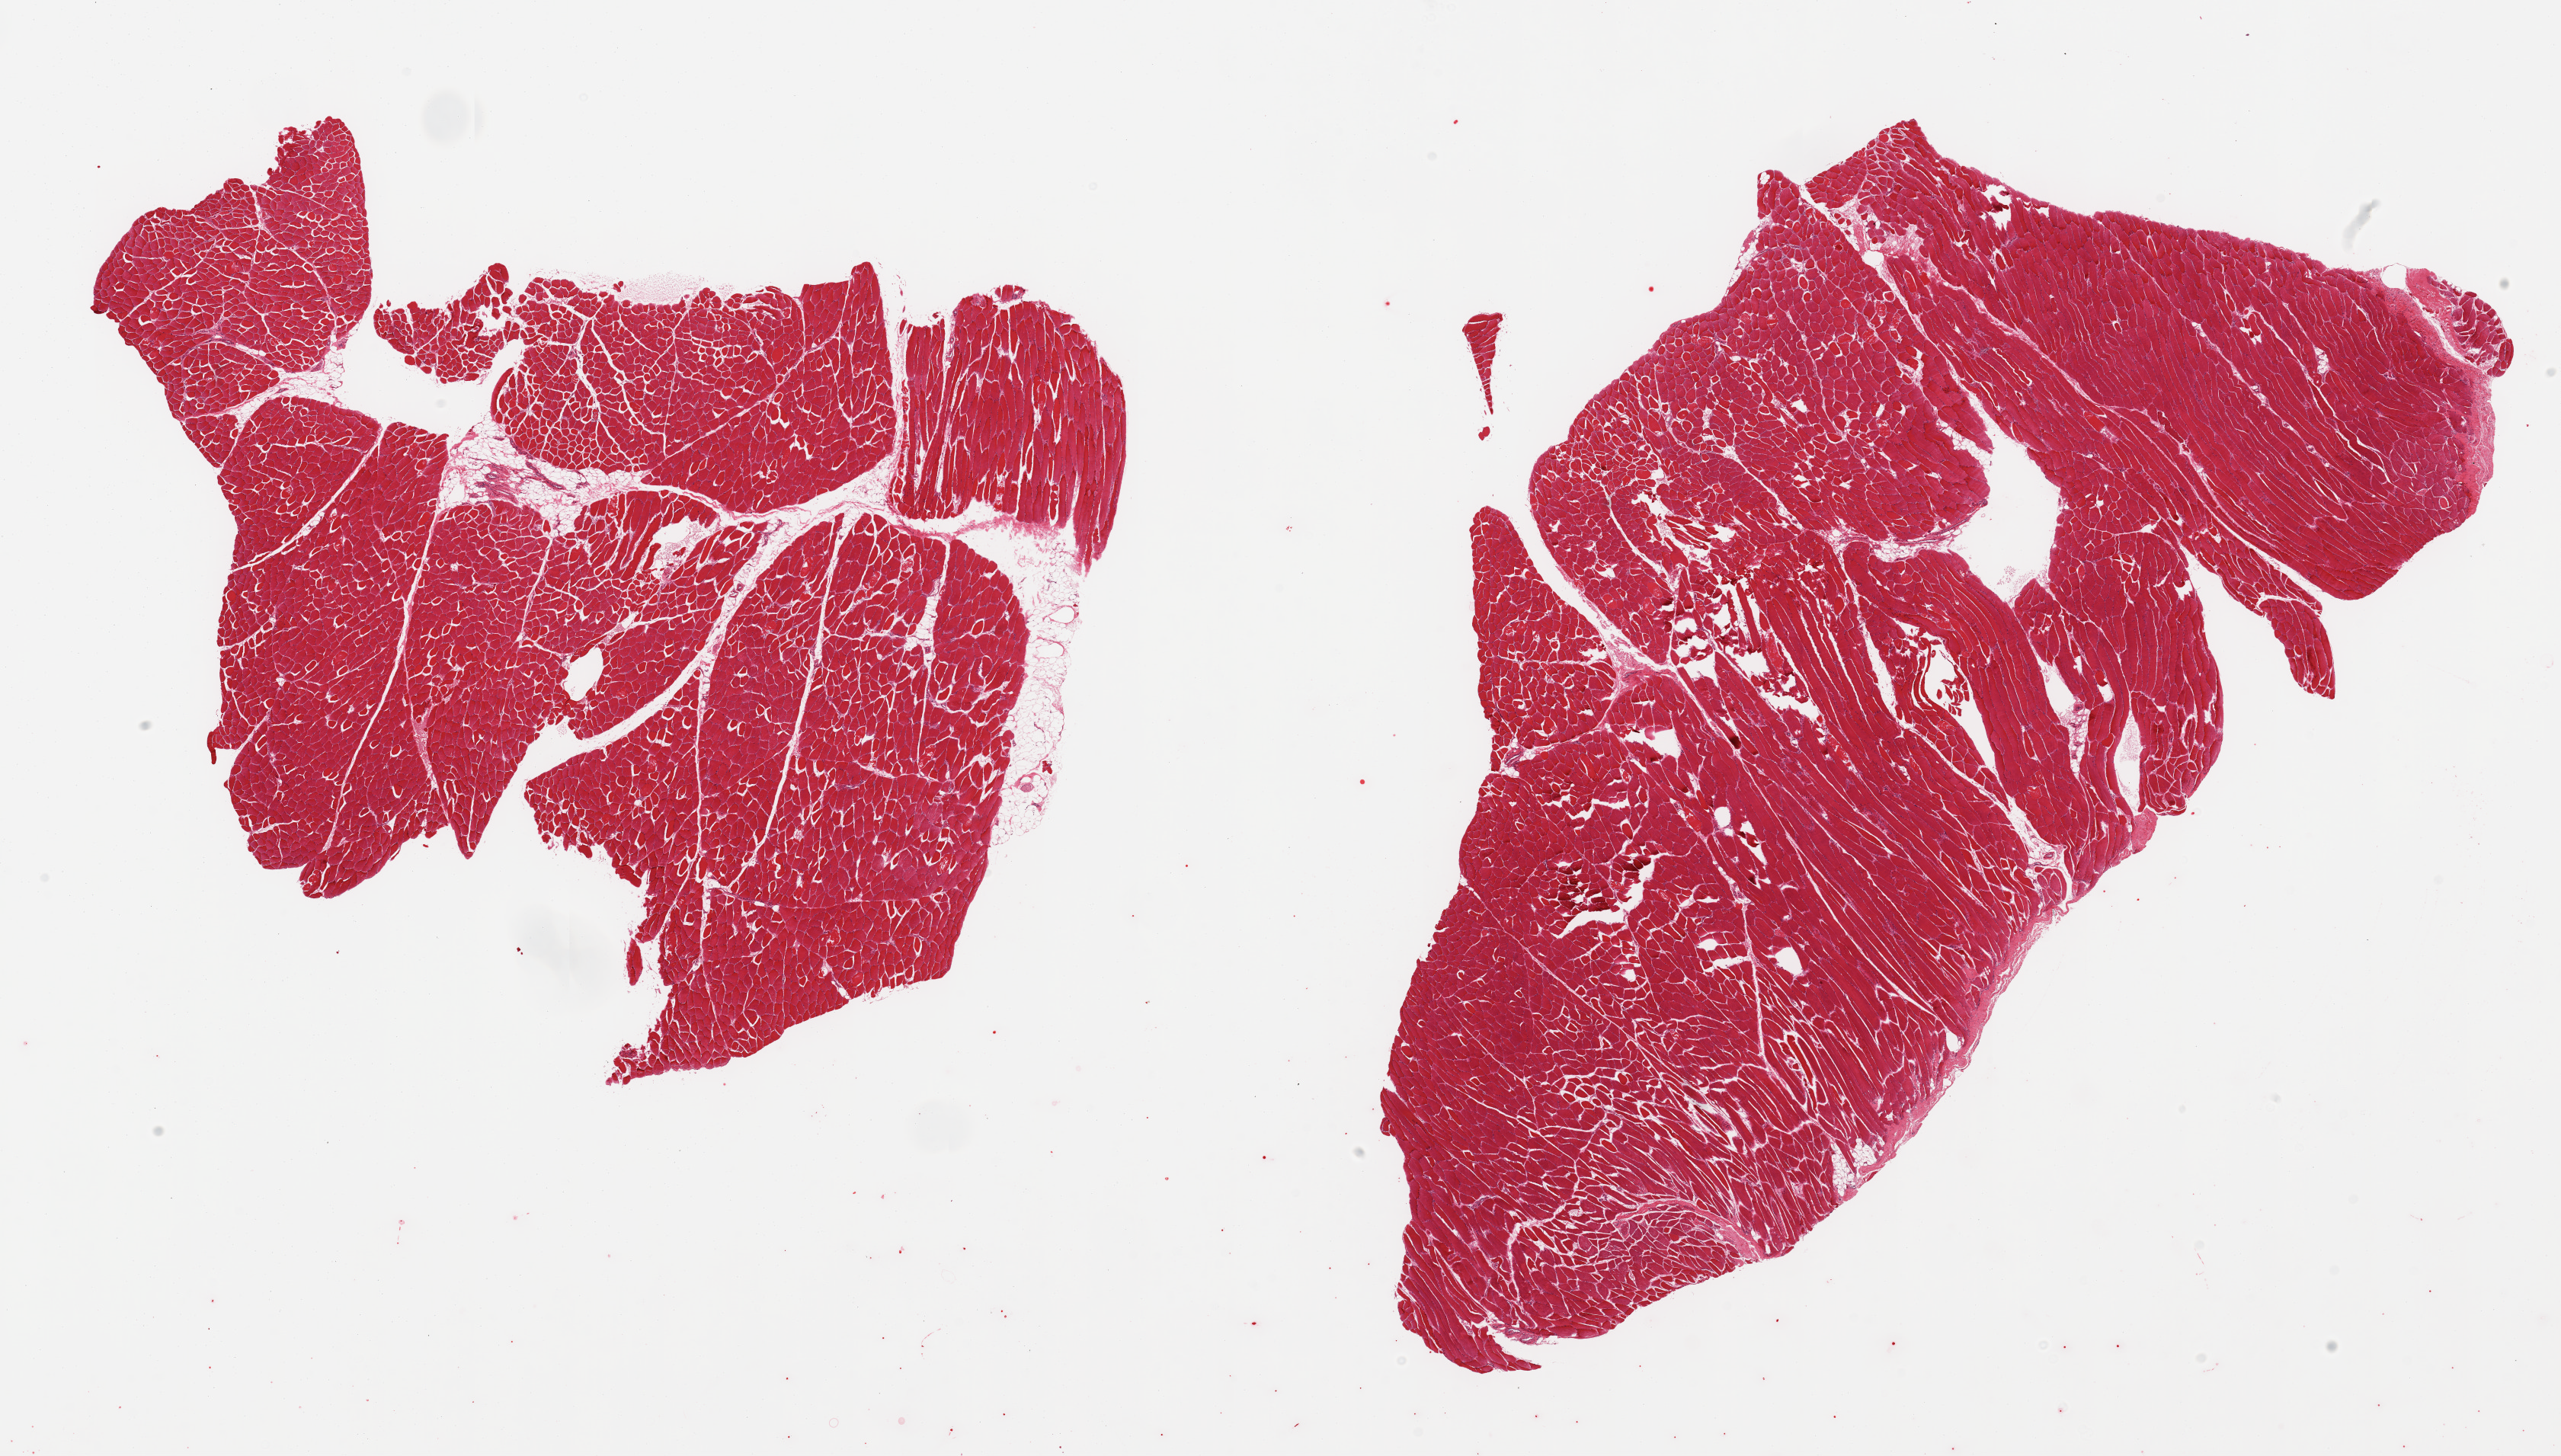
Whole-slide image, H&E stain — whole scanned area (about 26.6 x 15.1 mm, slide scanned at 20x) shown as a low-resolution overview; PAXgene-fixed paraffin-embedded (PFPE) section; target tissue: skeletal muscle; tissue donor sample. Donor sex: female.
- pathologist's review note for this sample: 2 pieces; minimal internal fat component